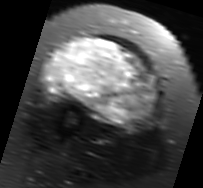
MRI of an extremity soft-tissue mass, one axial slice; slice 34 of 91 in the series (ordered by position); T2-weighted fat-saturated; MR volume resampled by the dataset authors to the PET/CT grid (not the native acquisition matrix); 3.27 mm slice thickness; 203 × 188 image matrix. Female patient. Case-level facts recorded for this patient, not image findings: histological type: malignant solitary fibrous tumor; grade: intermediate; site of the primary tumour: right thigh.
Annotated regions visible in this slice (expert contour drawn on MRI and transferred to this co-registered scan by the dataset authors):
- gross tumour volume including surrounding oedema: bounding box [x1, y1, x2, y2] px = [40, 37, 159, 130]
- gross tumour volume (mass): [47, 37, 157, 125]